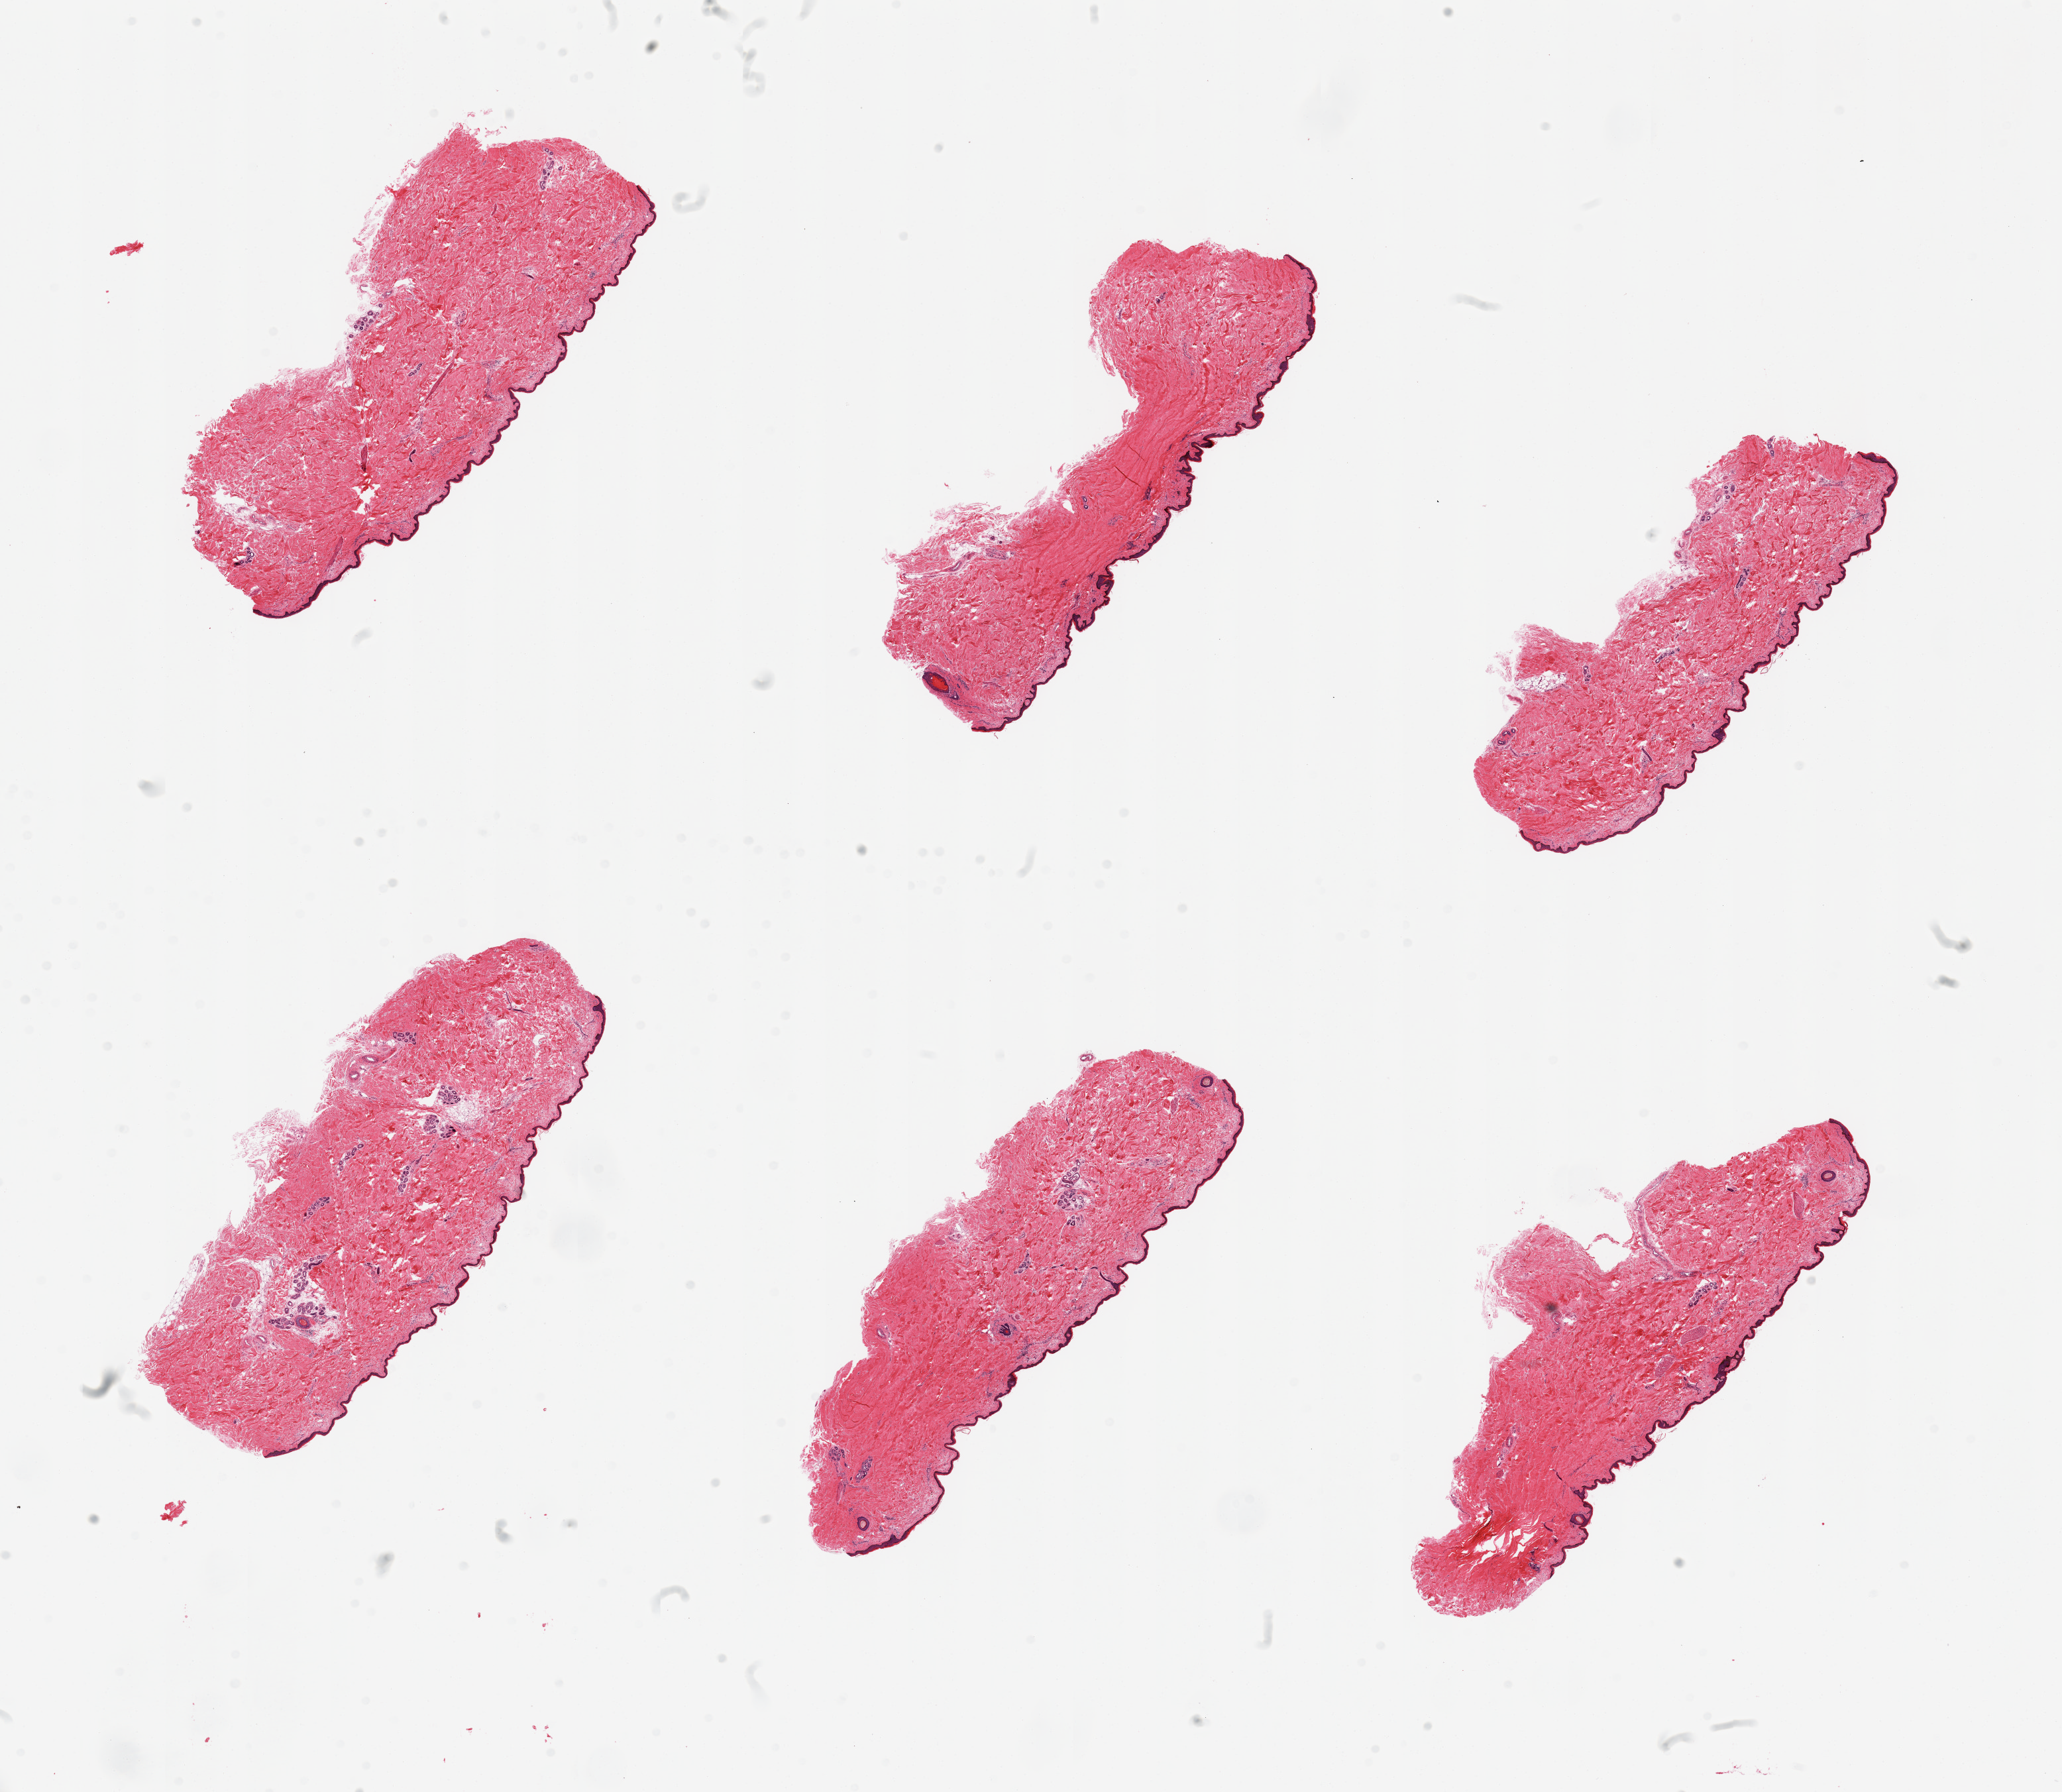
Whole-slide image, H&E stain, low-resolution overview of the scanned area, about 24.6 x 21.4 mm (acquisition: 20x scan), PAXgene-fixed, paraffin-embedded tissue, target tissue: skin of lower leg, tissue donor sample. Donor sex: male.
- reviewer comment on this tissue sample: 6 pieces, minimal dermal fat